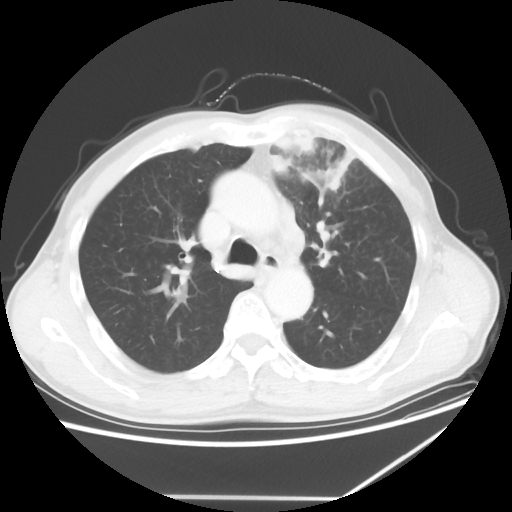
Chest CT, one axial slice. Position 43 of 64 along the scan axis. Reconstruction kernel STANDARD. 100 kVp. Lung window (W 1500 / L -600 HU). 5 mm slice thickness. 512 × 512 image matrix, field of view 383 × 383 mm. Patient: male, 64 years. Case-level facts recorded for this patient, not image findings: clinical TNM (as recorded): T1c N1 M1; histopathological grade: G2.
Outlined on this slice (rectangle marked by the reading radiologist):
- lung tumour (recorded histology: squamous cell carcinoma): box from (x=254, y=118) to (x=375, y=218) px